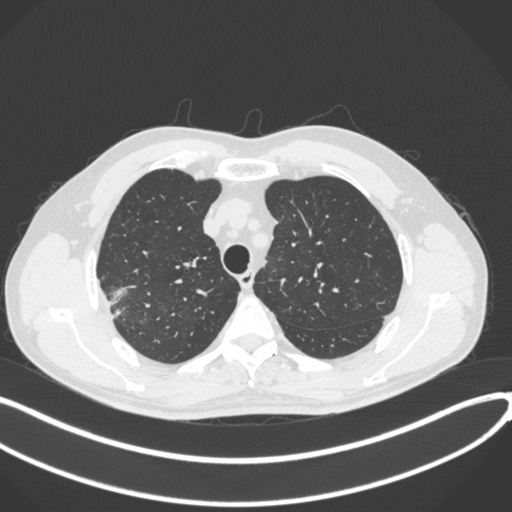
Chest CT, one axial slice; position 332 of 381 along the scan axis; lung window (W 1500 / L -600 HU); 512 × 512 image matrix, field of view 400 × 400 mm. Patient: male, 62 years. From the clinical record (not read from this slice): clinical TNM (as recorded): T1c N0 M0; histopathological grade: G2-3.
Annotated regions visible in this slice (rectangle marked by the reading radiologist):
- lung tumour (recorded histology: adenocarcinoma): bounding box [x1, y1, x2, y2] px = [106, 282, 132, 322]